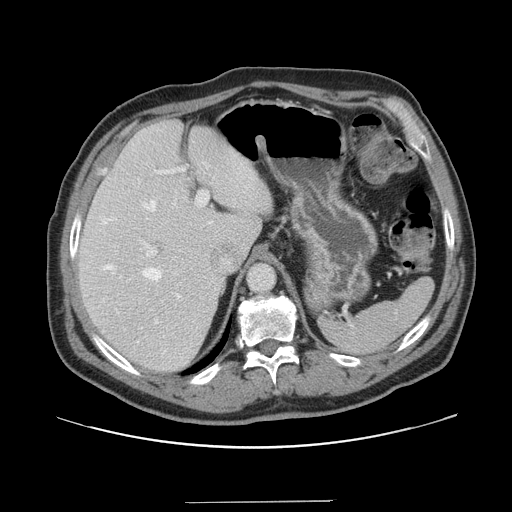
Contrast-enhanced abdominal CT, one axial slice; slice 108 of 151 in the series (ordered by position); intravenous contrast given; soft-tissue window (W 400 / L 40 HU); 2.5 mm slice thickness; 512 × 512 image matrix, field of view 399 × 399 mm. Male patient, age 63 years. From the clinical record (not read from this slice): diagnosis: colorectal cancer liver metastases, imaged before liver resection.
Structures marked on this image (outlined manually by an expert reader):
- hepatic veins: bounding box (x1, y1, x2, y2) in pixels: (102, 200, 212, 280)
- liver: (78, 120, 272, 373)
- planned liver remnant (the part of the liver to remain after resection): (78, 120, 264, 373)
- portal vein (with intrahepatic branches): (143, 168, 209, 299)